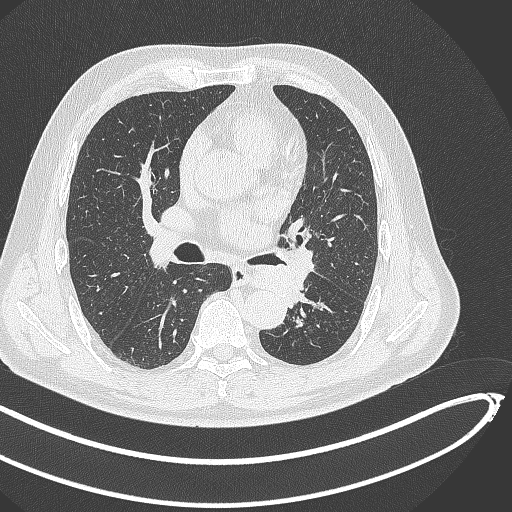
Chest CT, one axial slice. Slice 257 of 468 in the series (ordered by position). 120 kVp. Lung window (W 1500 / L -600 HU). 1 mm slice thickness. 512 × 512 image matrix. Male patient, age 64 years. From the clinical record (not read from this slice): clinical TNM (as recorded): T1c N0 M0; histopathological grade: G2.
Annotated regions visible in this slice (bounding box drawn by a radiologist):
- lung tumour (recorded histology: squamous cell carcinoma): bounding box [x1, y1, x2, y2] px = [249, 259, 315, 305]